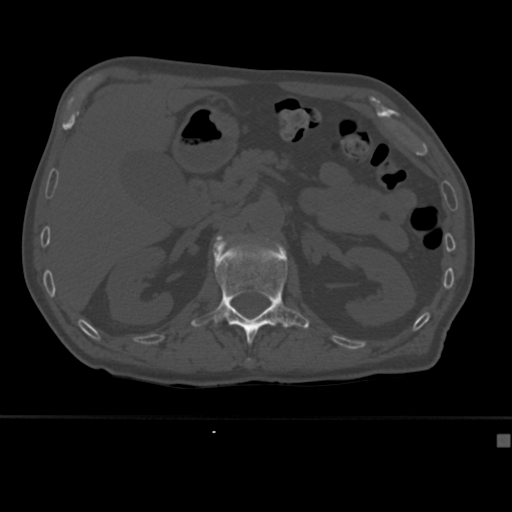
CT including the spine, one axial slice. Reconstruction kernel Br40s. 120 kVp. Bone window (W 1800 / L 400 HU). 1.5 mm slice thickness. 512 × 512 image matrix, field of view 337 × 337 mm. Patient: male, 64 years. Case-level facts recorded for this patient, not image findings: primary cancer: uterus.
Structures marked on this image (semi-automatically segmented with operator editing):
- L1 vertebra: bounding box <191,236,310,363> (left, top, right, bottom; pixels)